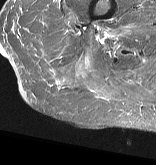
MRI of an extremity soft-tissue mass, one axial slice; position 11 of 57 along the scan axis; STIR; MR volume resampled by the dataset authors to the PET/CT grid (not the native acquisition matrix); 3.27 mm slice thickness; 156 × 165 image matrix. Female patient. From the clinical record (not read from this slice): histological type: epithelioid sarcoma with vascular differentiation; site of the primary tumour: right buttock.
Structures marked on this image (expert contour drawn on MRI and transferred to this co-registered scan by the dataset authors):
- gross tumour volume (mass): bounding box <65,46,71,49> (left, top, right, bottom; pixels)